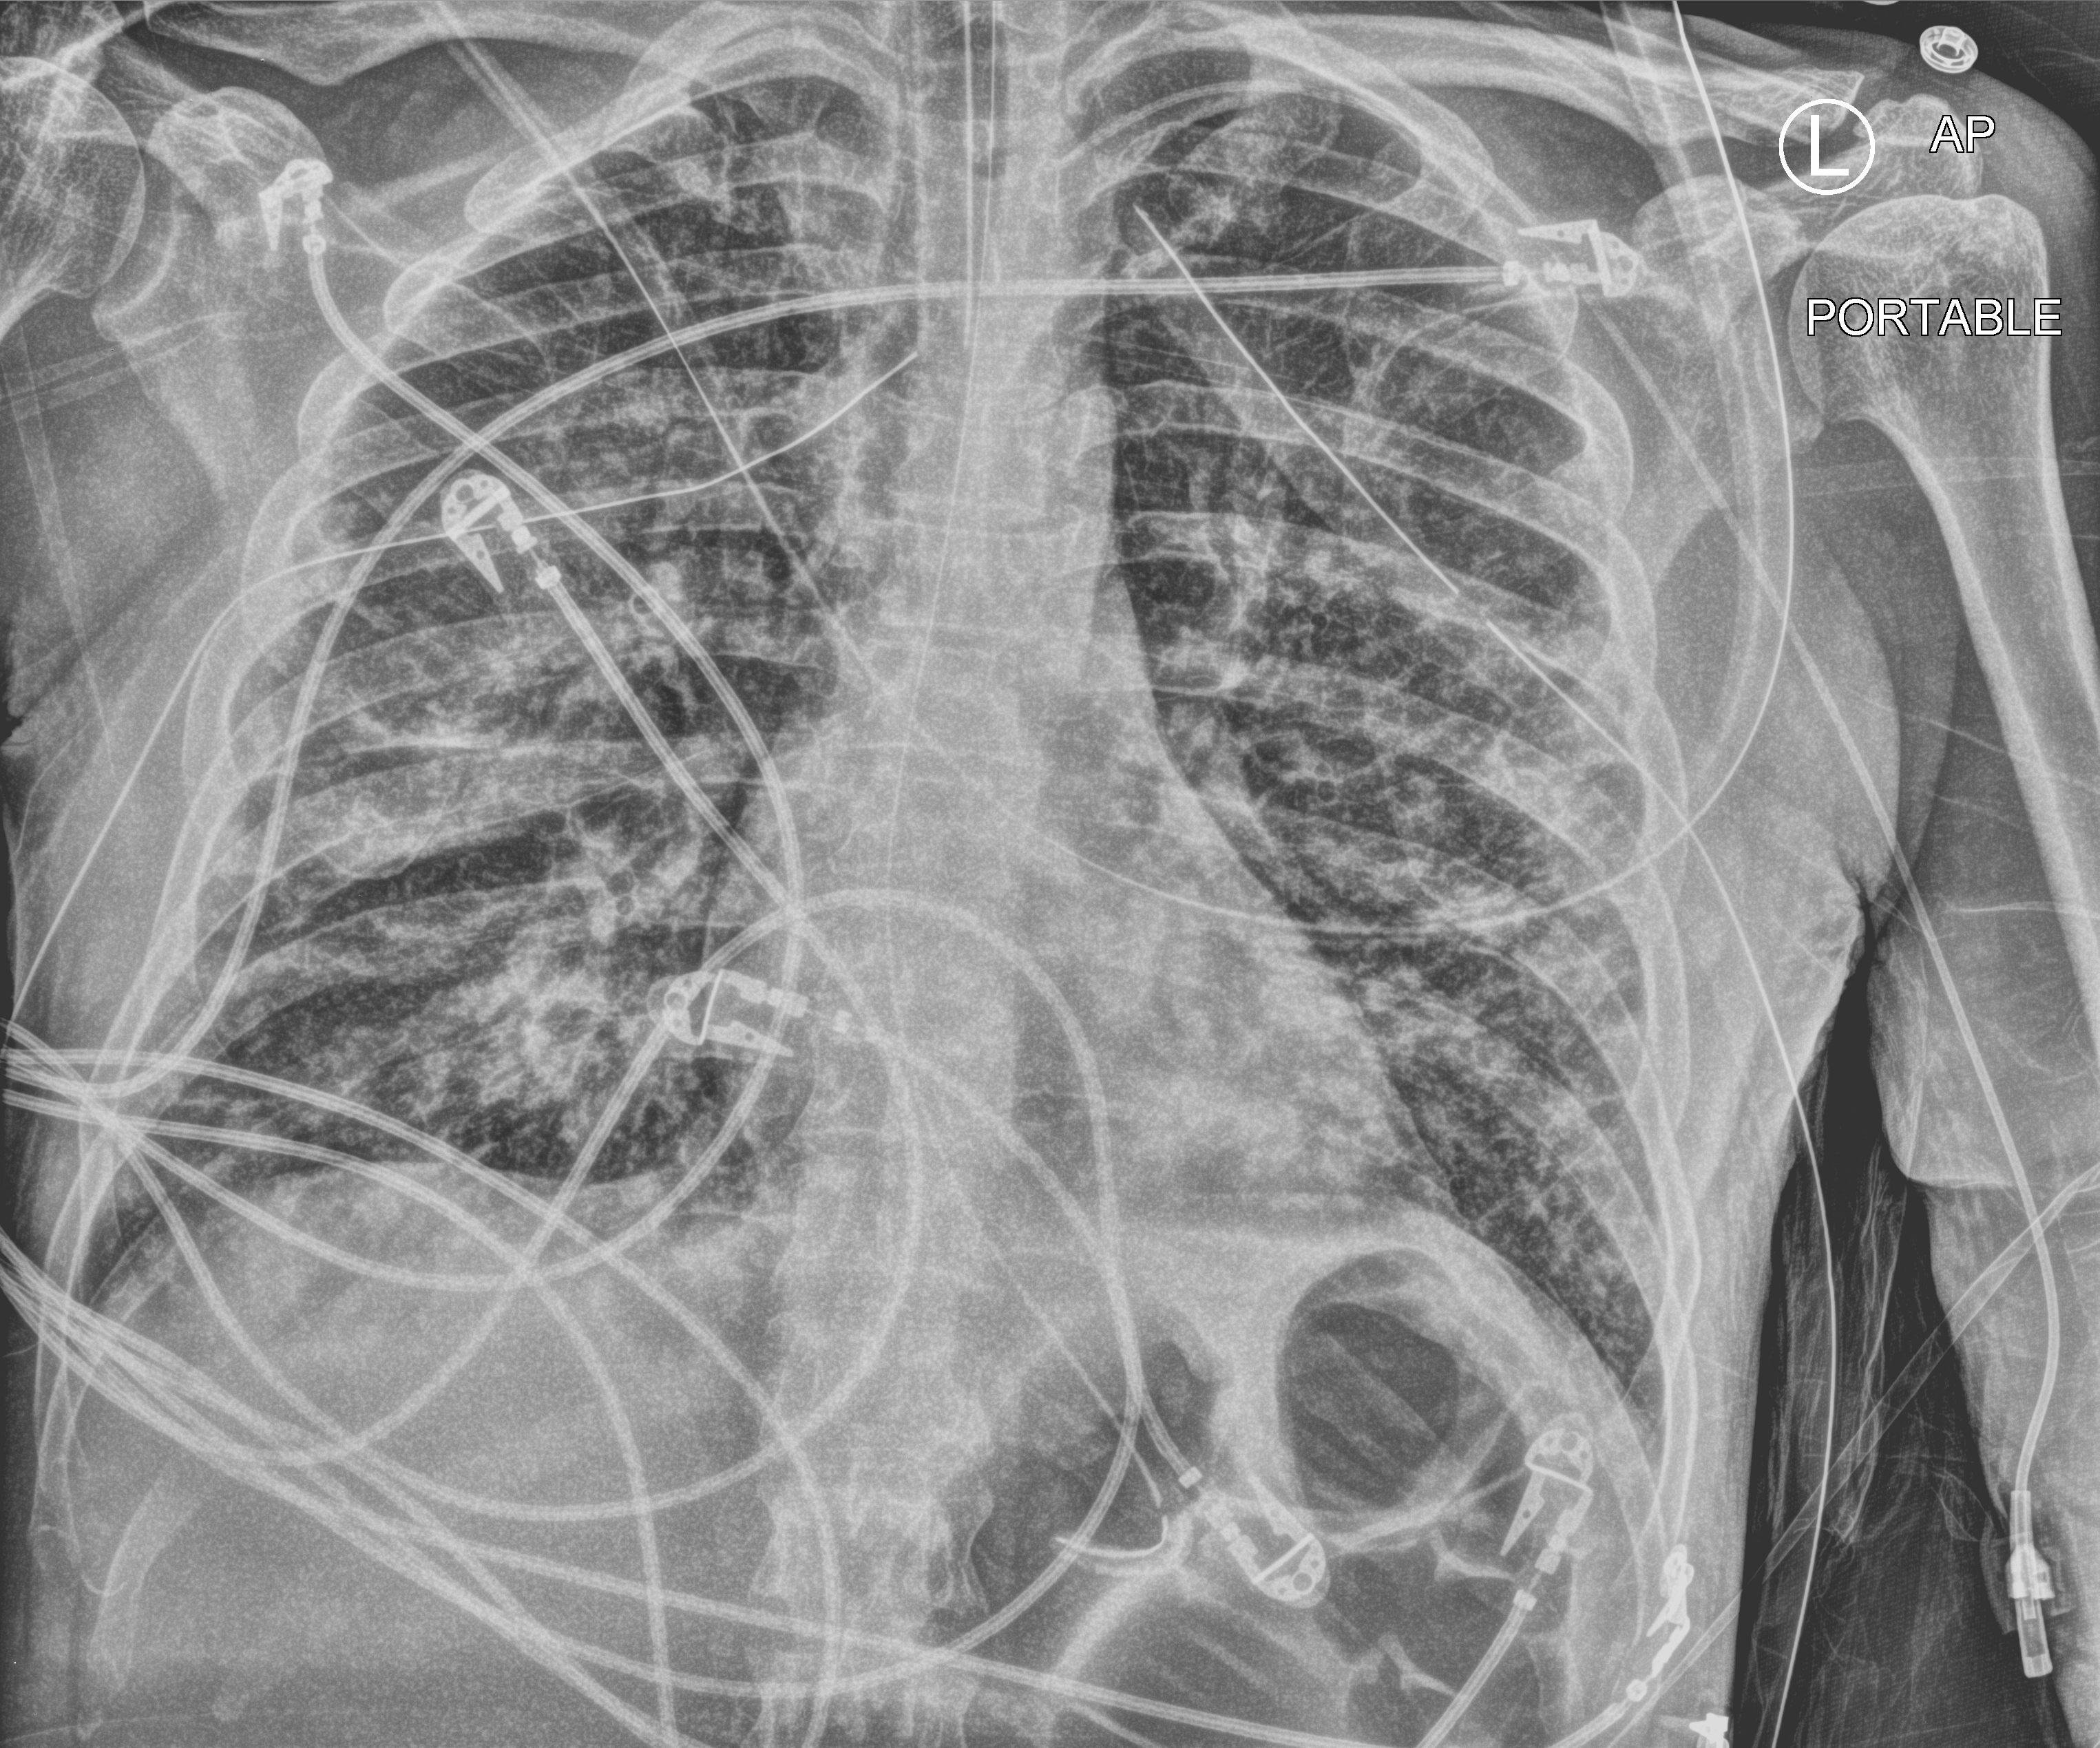
Chest X-ray (portable); anteroposterior (AP) projection. Male patient hospitalised with COVID-19, age 18–59 years.
Admission-level facts for this patient (not findings on this image; timing relative to this image not recorded): admitted to intensive care during this hospital stay: yes.